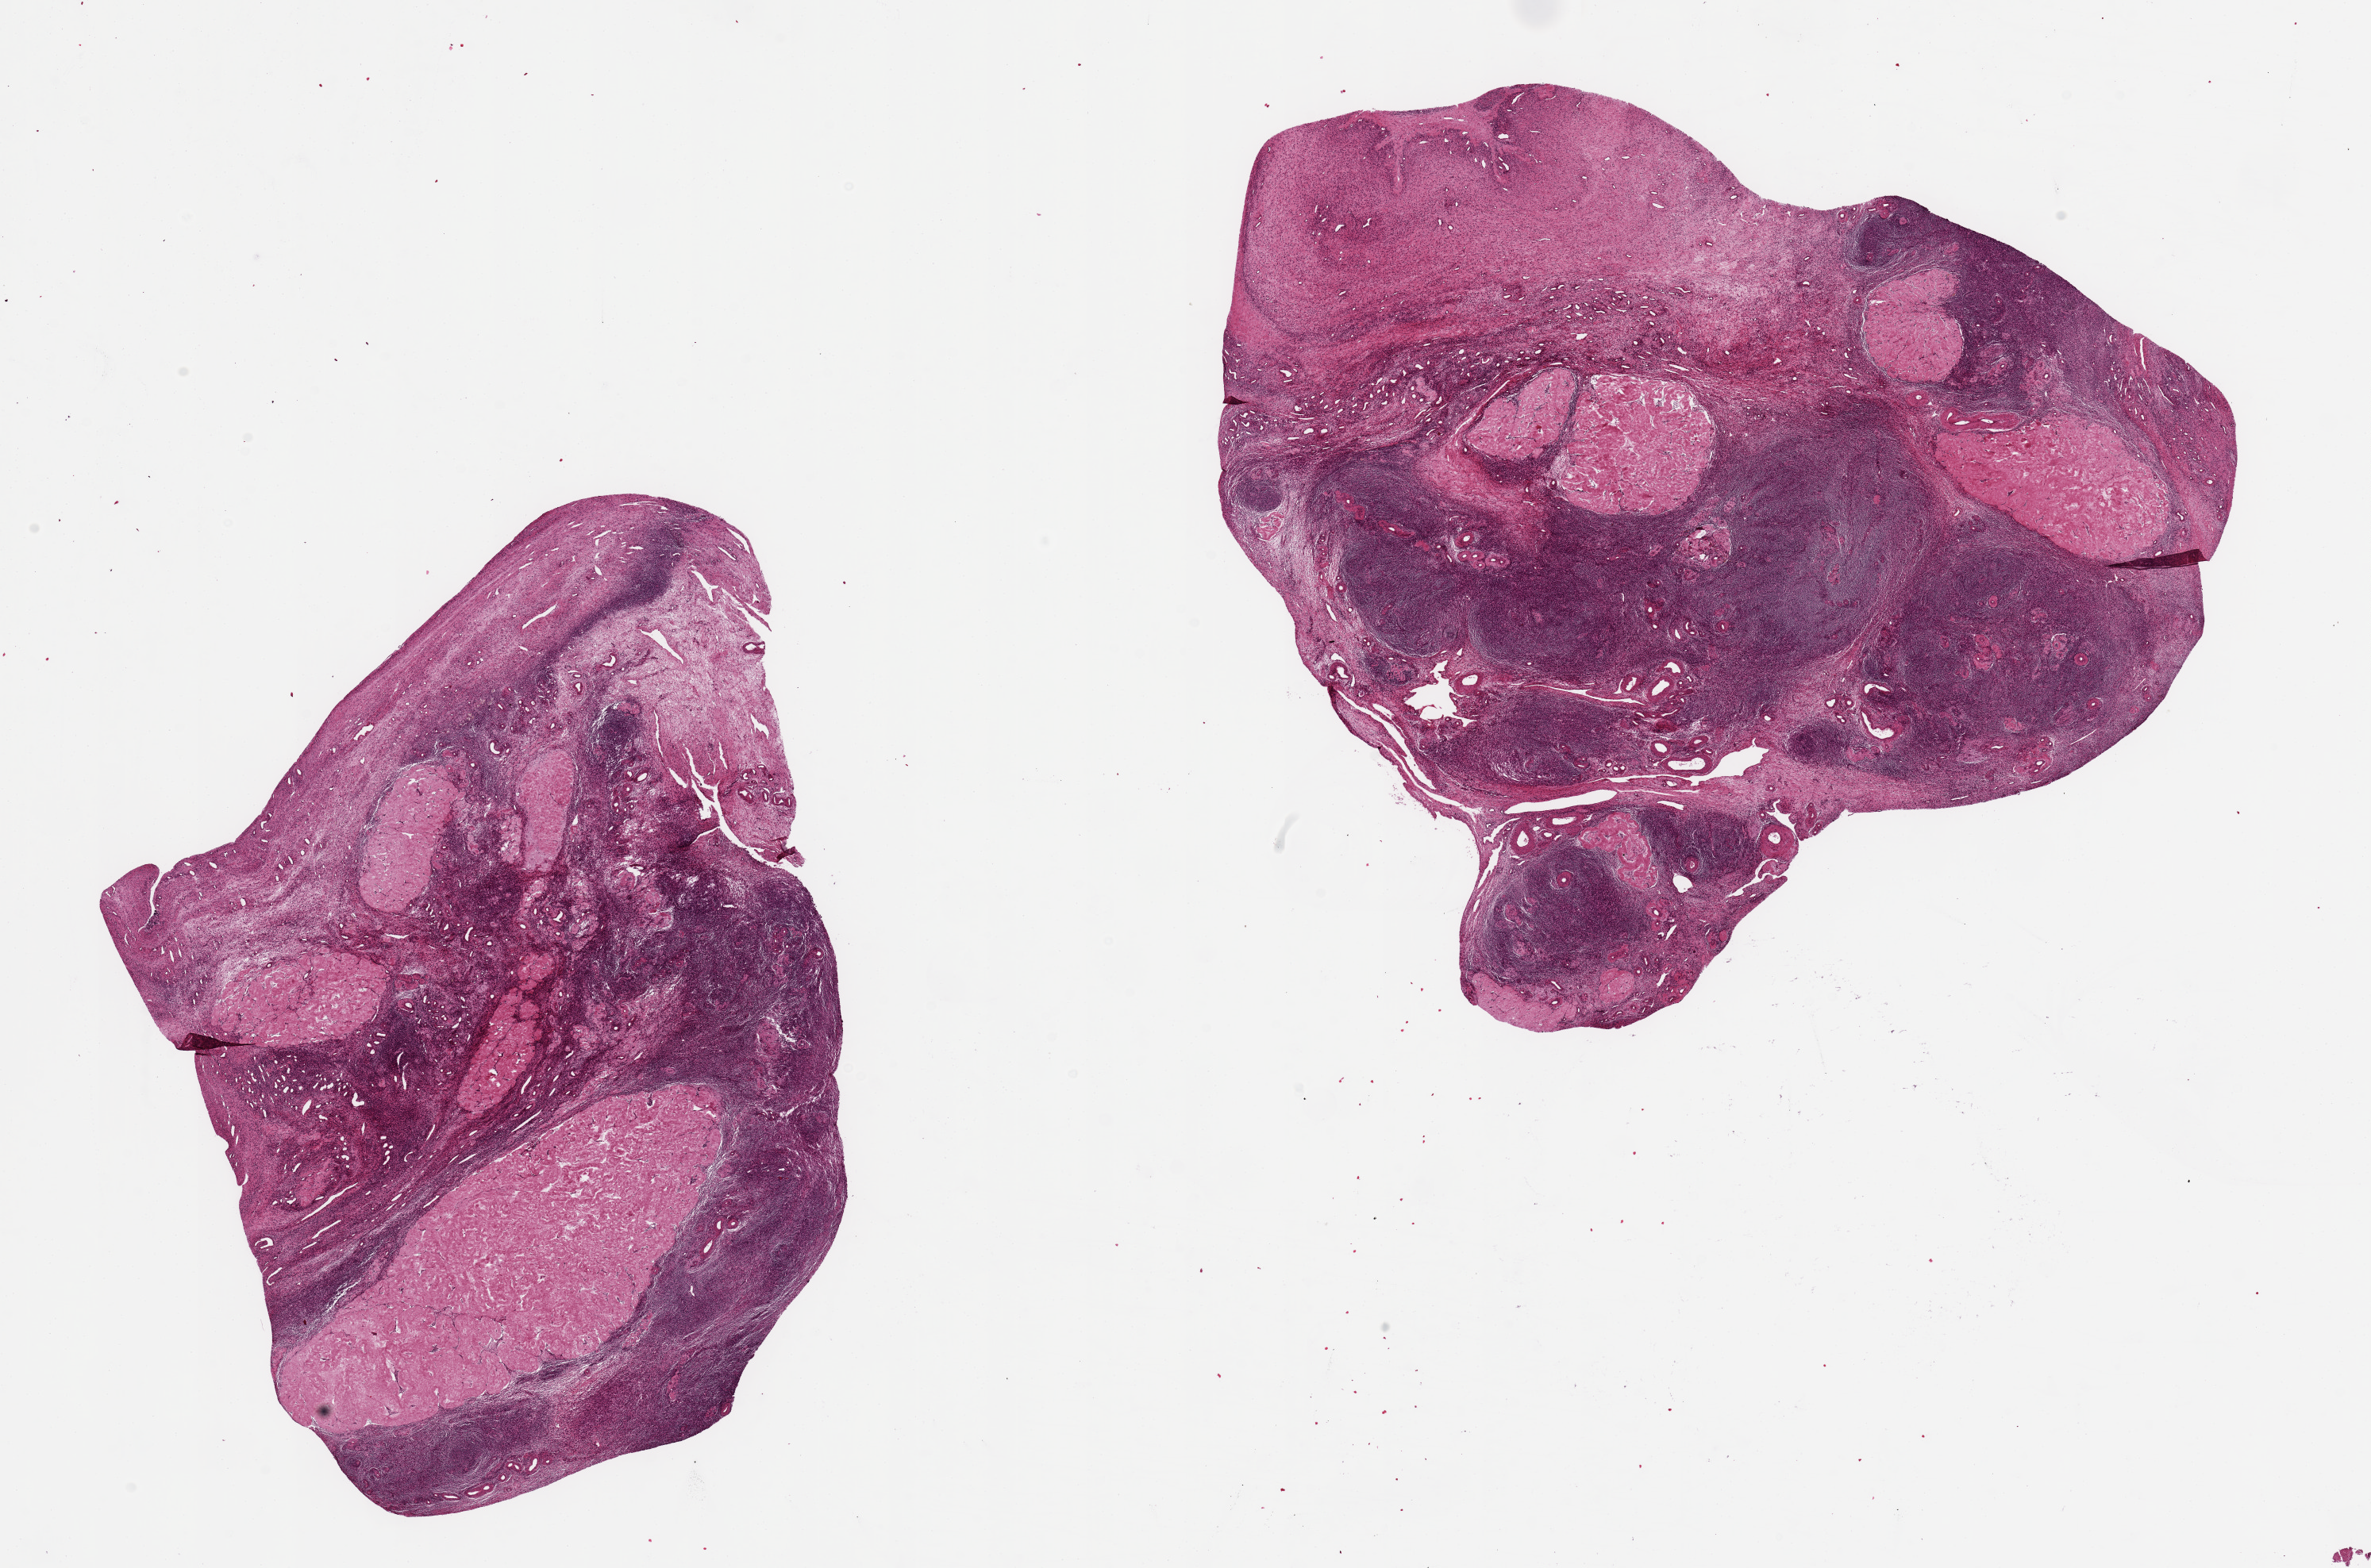
Digitized H&E-stained section, brightfield — shown as a low-resolution overview of the whole scanned area (about 23.6 x 15.6 mm, acquisition: 20x scan), PAXgene-fixed, paraffin-embedded tissue, section of ovary (target tissue), tissue donor sample.
* pathologist's review note for this sample: 2 pieces 10x10 & 10x7 mm; atrophic, no ova, corpora albicantia